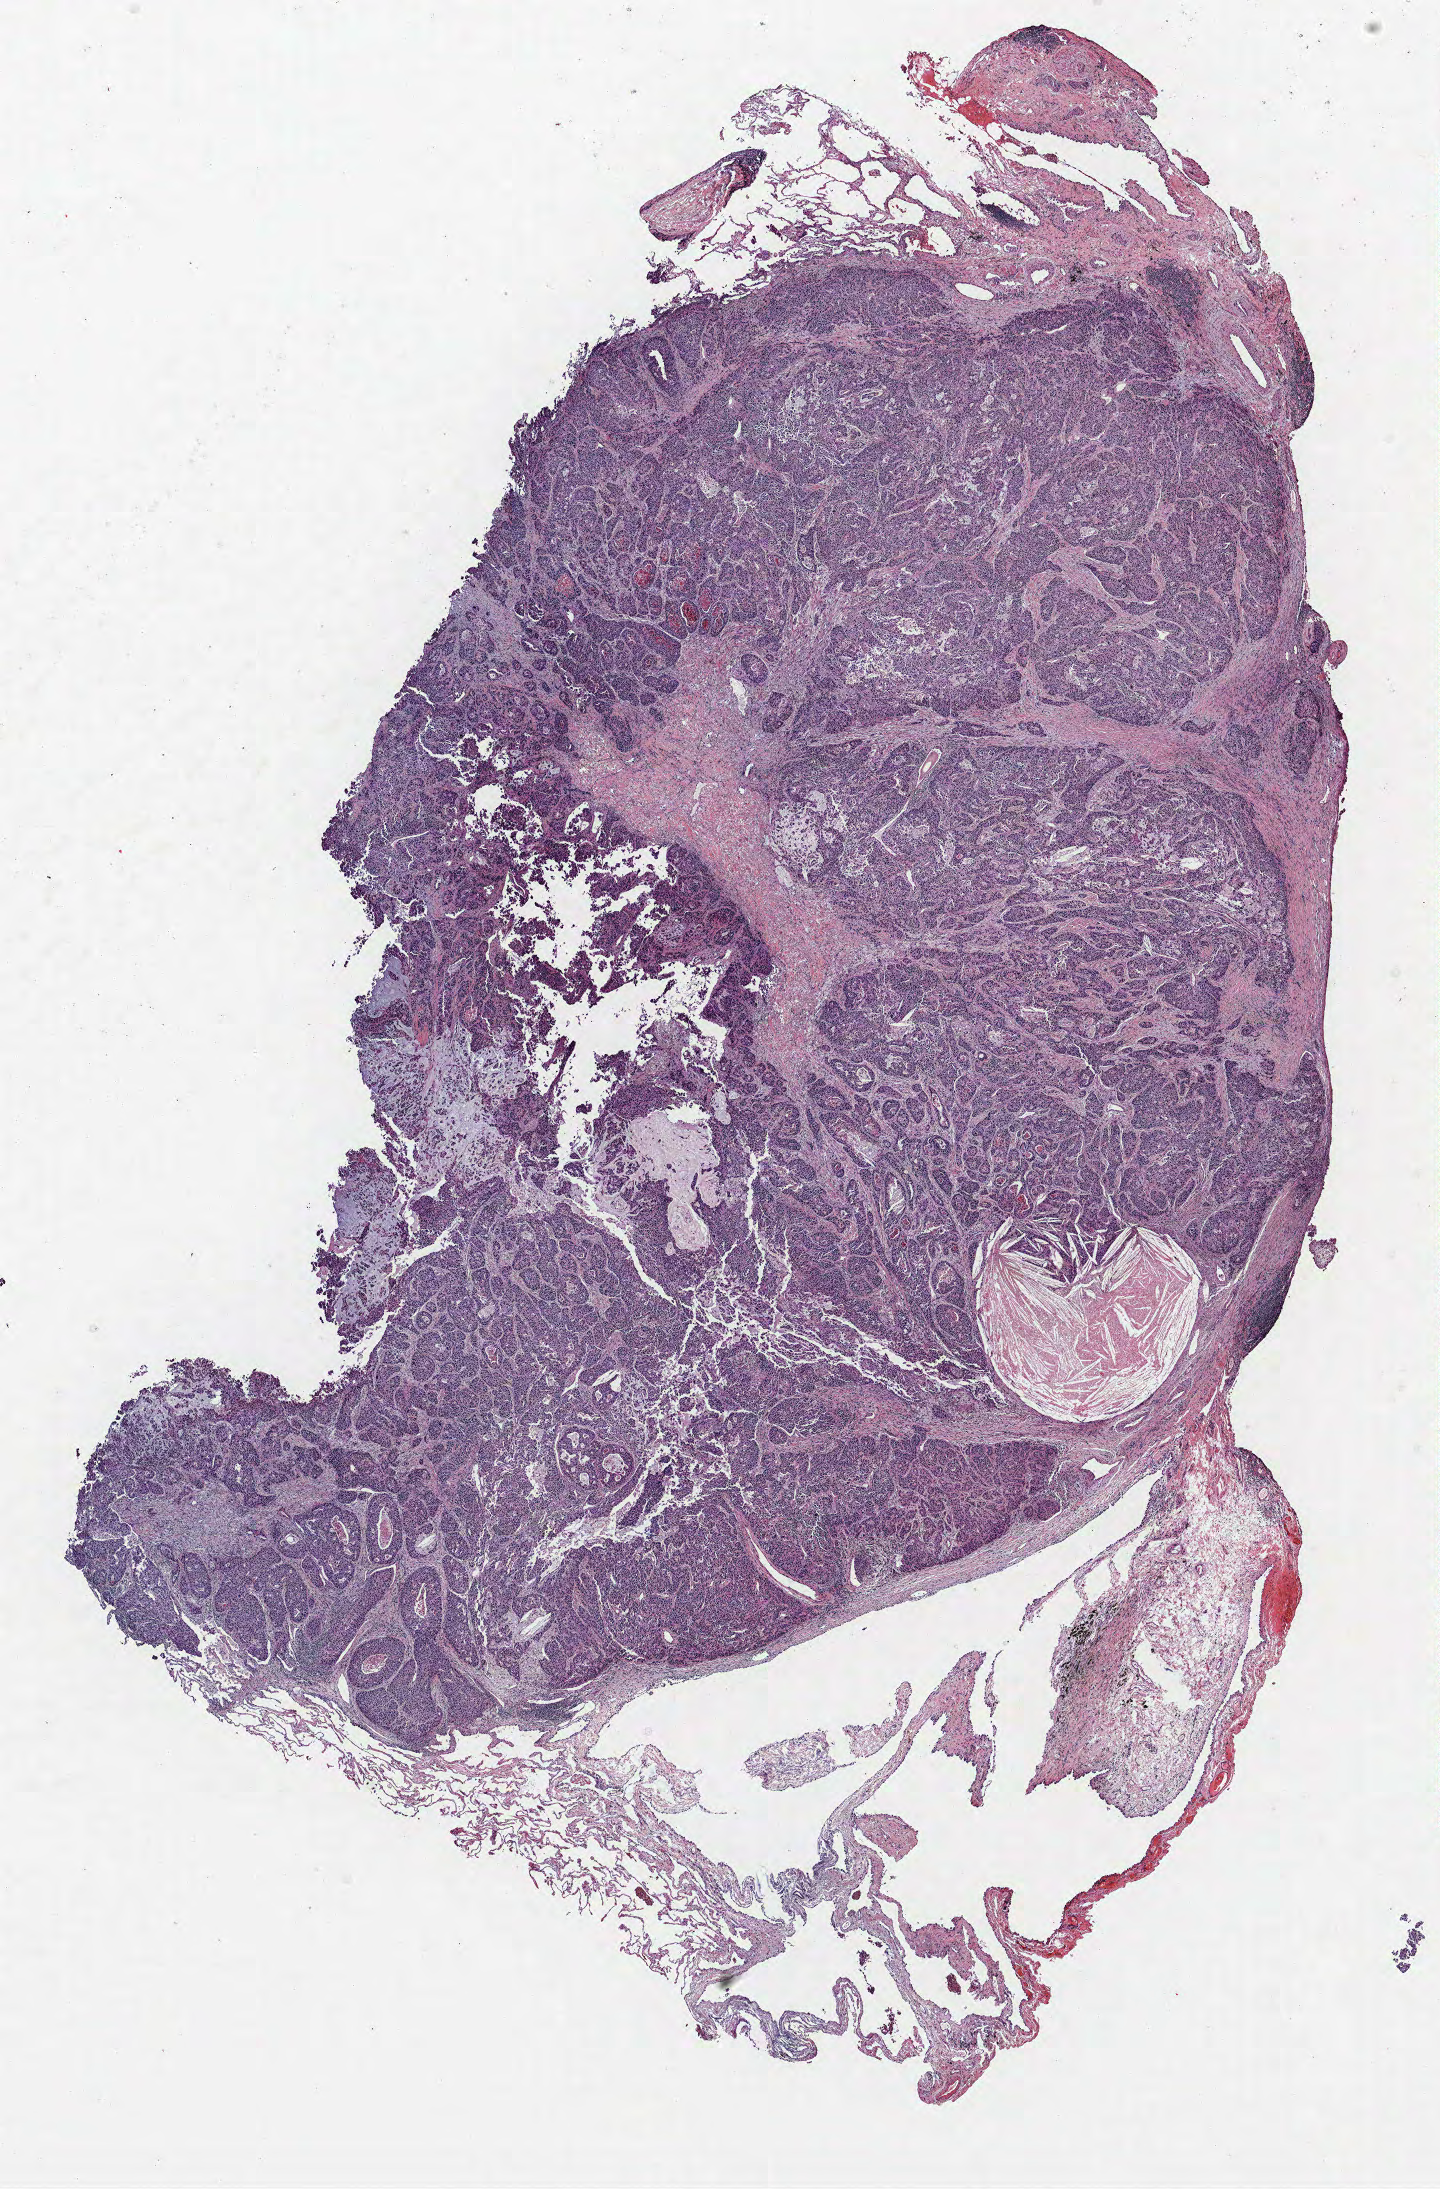
Whole-slide histology image, H&E — low-resolution overview of the scanned area, about 11.5 x 17.5 mm (from a 40x scan). Formalin-fixed paraffin-embedded (FFPE) section. Lung. Female patient, aged 64 at enrolment. Current smoker at enrolment. Grade: poorly differentiated (G3).
Primary tumour location (clinical record): right upper lobe. Tumour size (pathology): 15 mm. Participant's lung-cancer diagnosis: Adenocarcinoma, NOS (ICD-O-3 8140/3). Stage (AJCC 6th edition): IB.